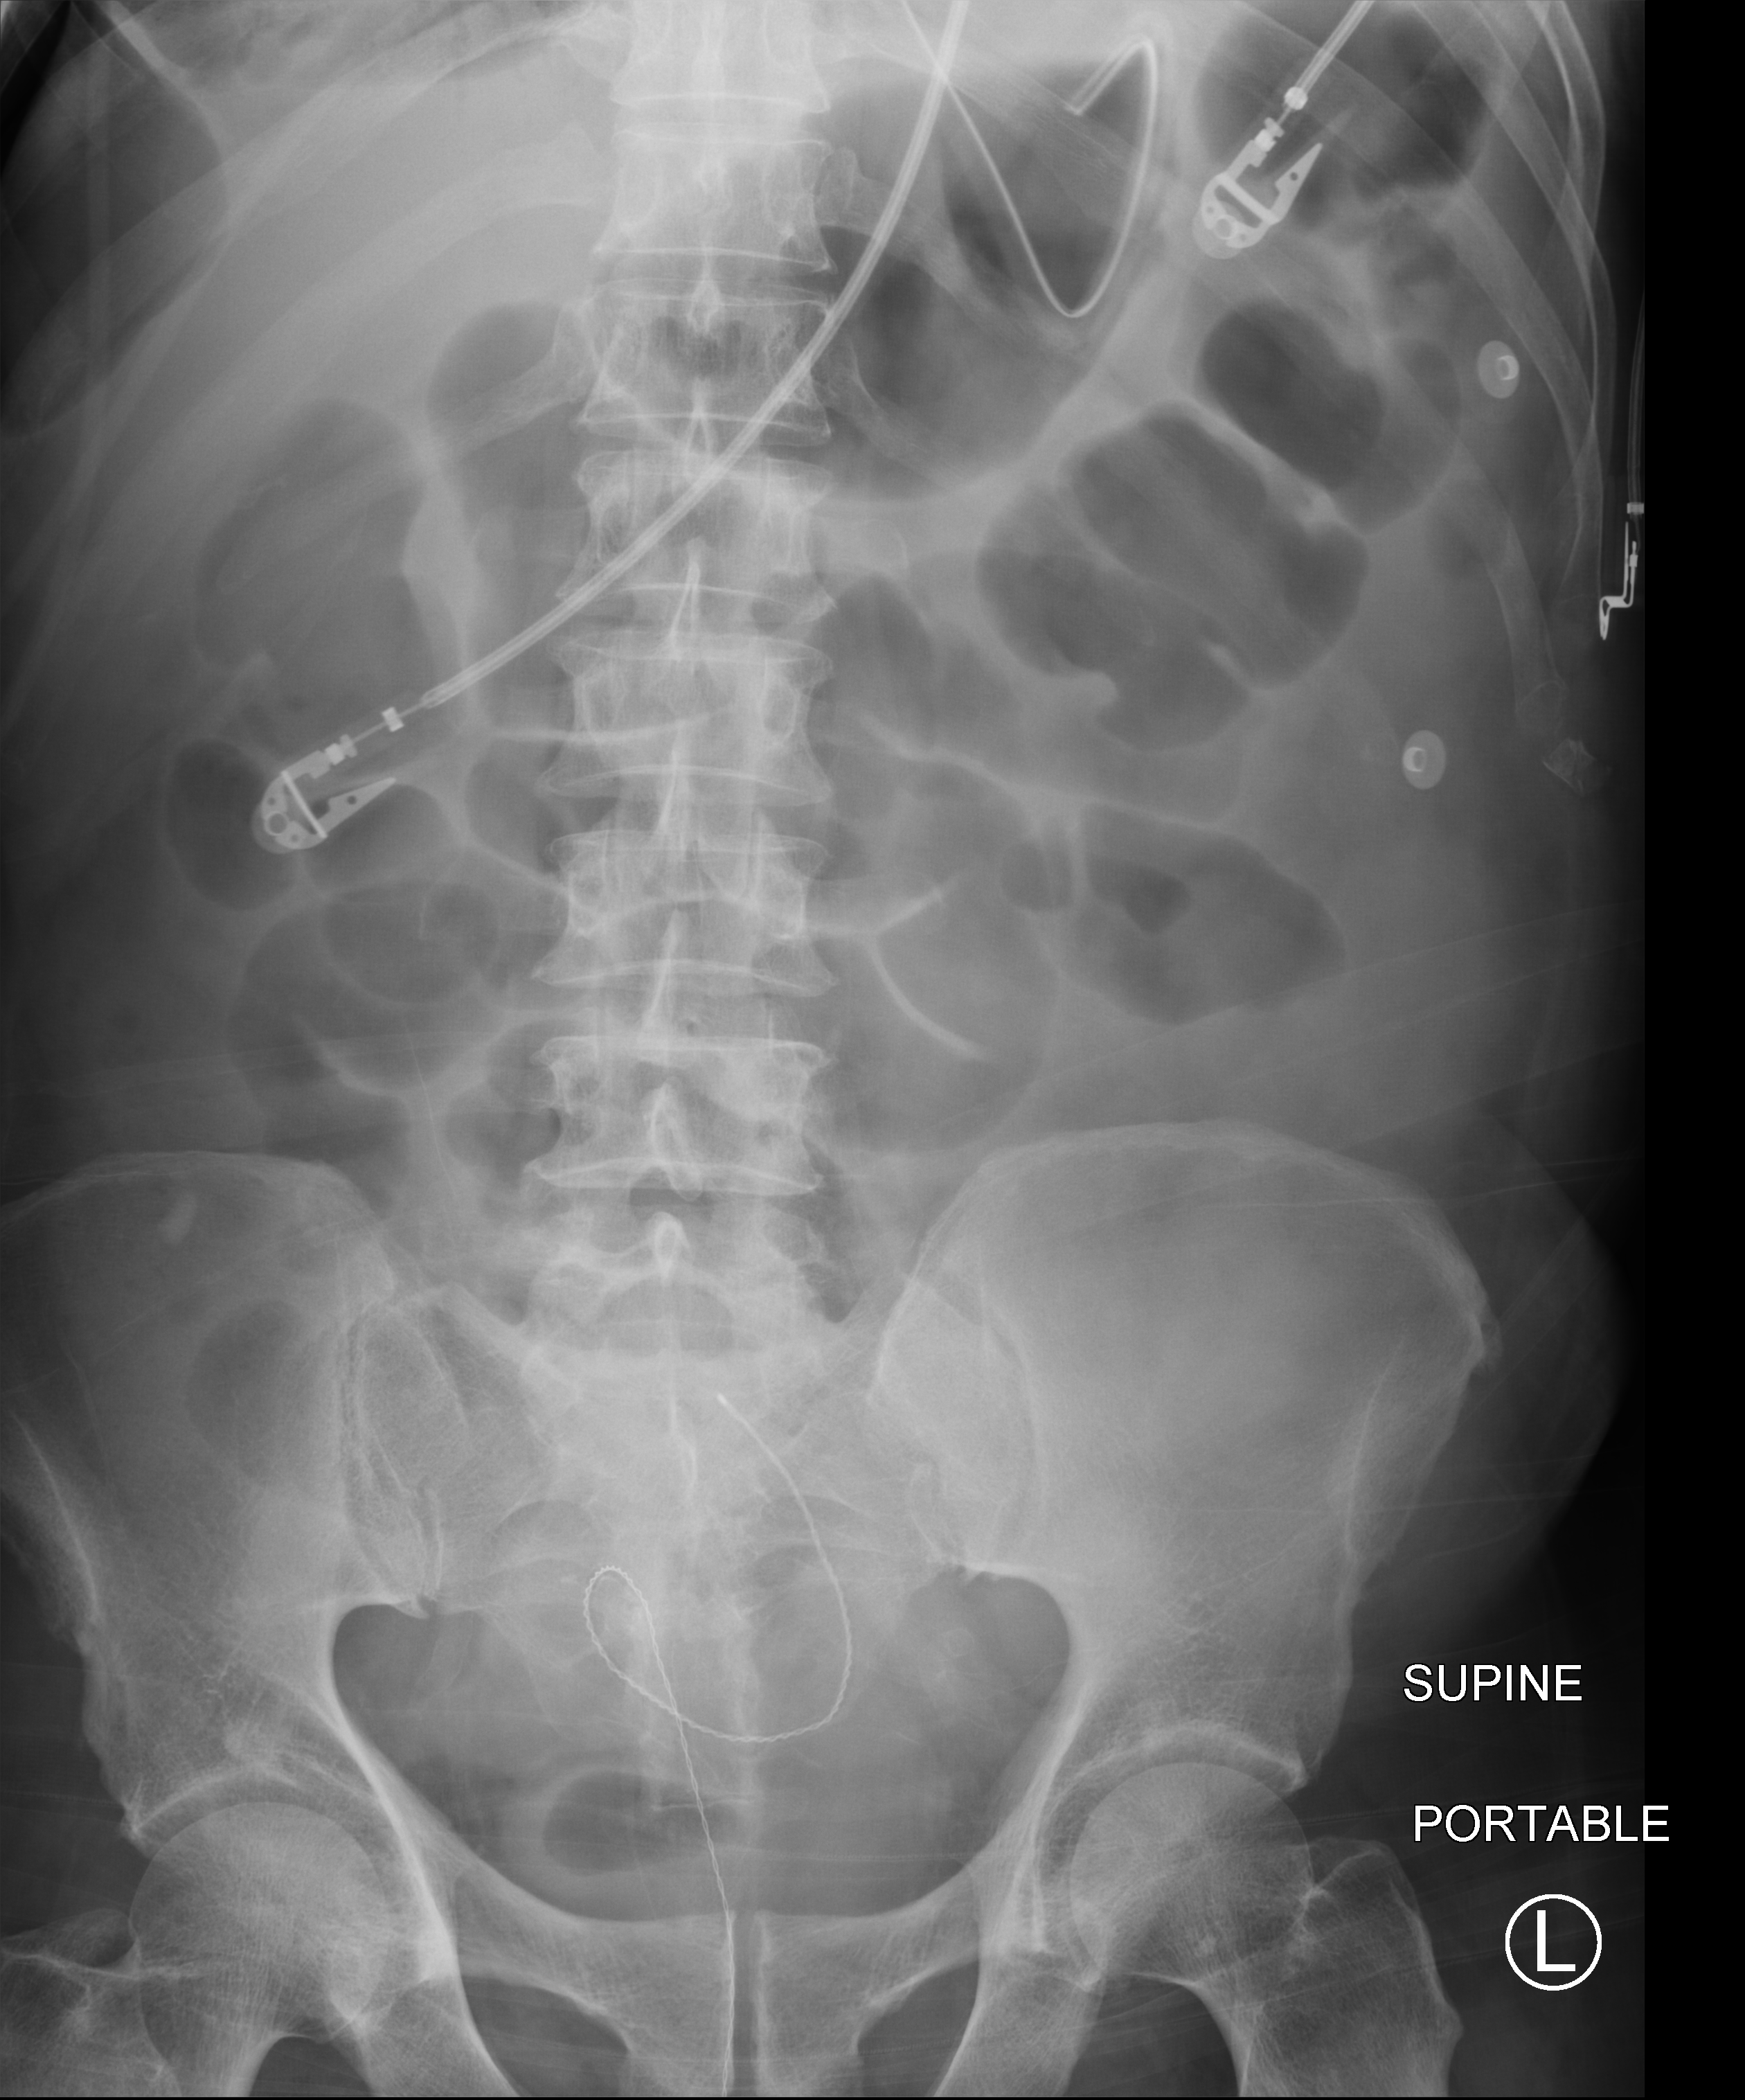
Portable abdomen radiograph, anteroposterior (AP) projection. Patient hospitalised with COVID-19; male, aged 60–74 years.
From the hospital-stay record, not from the radiograph (when in the stay this image was taken is not recorded): mechanically ventilated during this hospital stay: yes; chronic kidney disease (admission record): no; COPD (admission record): no.